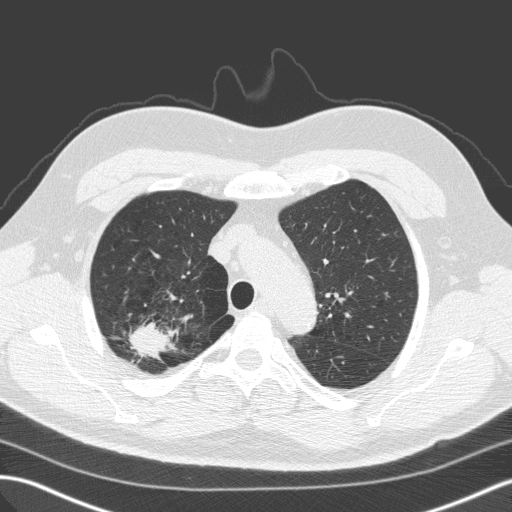
Chest CT (low-dose screening protocol), one axial image. First (baseline) screen. Lung window (W 1500 / L -600 HU). Standard (soft-tissue) reconstruction kernel (C). 120 kVp. Male participant, aged 59 years at enrolment. Former smoker at enrolment.
Expert reader's lesion annotation, bounding box [x1, y1, x2, y2] px = [117, 310, 178, 370]. The exam's reader record, not a measurement of the box and not confirmed to be the same lesion: non-calcified nodule or mass ≥4 mm, right upper lobe, 28 × 25 mm, spiculated (stellate) margins, soft tissue attenuation. Official screen result: positive, change unspecified: nodule(s) >= 4 mm or enlarging nodule(s), mass(es), or other non-specific abnormalities suspicious for lung cancer. Participant outcome: lung cancer diagnosed 64 days after this screen — large cell carcinoma, NOS, right upper lobe, undifferentiated (G4), stage IA (AJCC 6th edition), 25 mm at pathology.